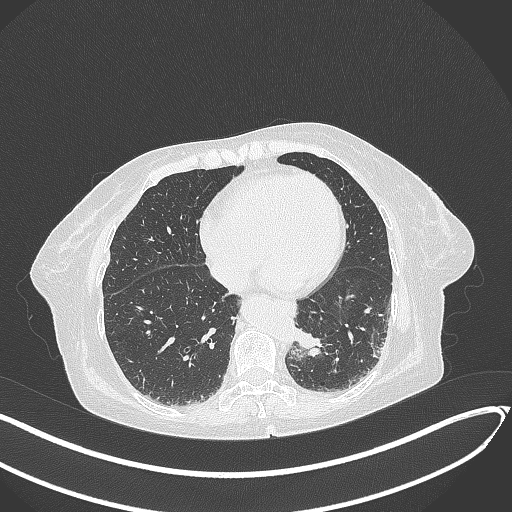
Chest CT, one axial slice. Position 68 of 324 along the scan axis. 120 kVp. Lung window (W 1500 / L -600 HU). 1 mm slice thickness. 512 × 512 image matrix. Female patient, age 82 years. Case-level facts recorded for this patient, not image findings: clinical TNM (as recorded): T1b N0 M1.
Structures marked on this image (rectangle marked by the reading radiologist):
- lung tumour (recorded histology: adenocarcinoma): bounding box (x1, y1, x2, y2) in pixels: (294, 326, 326, 355)